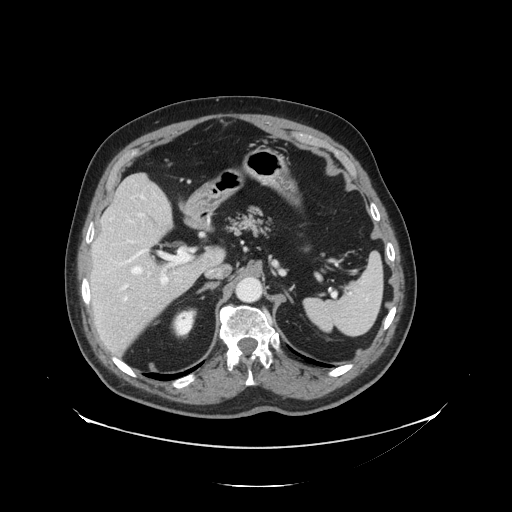
Contrast-enhanced abdominal CT, one axial slice; slice 87 of 138 in the series (ordered by position); reconstruction kernel STANDARD; intravenous contrast given; soft-tissue window (W 400 / L 40 HU); 512 × 512 image matrix. Male patient, age 77 years. Case-level facts recorded for this patient, not image findings: diagnosis: colorectal cancer liver metastases, imaged before liver resection; multiple liver metastases: no; largest metastasis: 1.5 cm; chemotherapy before resection: no.
Structures marked on this image (manually delineated by an expert):
- hepatic veins: bounding box [x1, y1, x2, y2] px = [123, 214, 142, 287]
- liver: [90, 175, 222, 356]
- planned liver remnant (the part of the liver to remain after resection): [92, 175, 218, 288]
- portal vein (with intrahepatic branches): [116, 249, 193, 301]